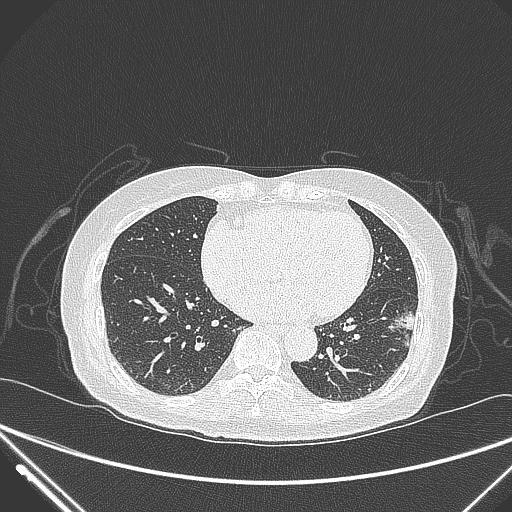
Chest CT, one axial slice. Position 114 of 310 along the scan axis. Lung window (W 1500 / L -600 HU). 1 mm slice thickness. 512 × 512 image matrix, field of view 377 × 377 mm. Female patient, age 82 years. From the clinical record (not read from this slice): clinical TNM (as recorded): T1c N0 M0.
Structures marked on this image (bounding box drawn by a radiologist):
- lung tumour (recorded histology: adenocarcinoma): bounding box (x1, y1, x2, y2) in pixels: (388, 303, 421, 353)